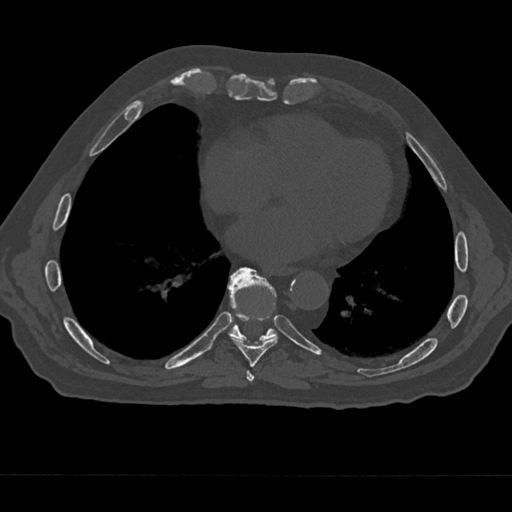
CT including the spine, one axial slice; slice 294 of 797 in the series (ordered by position); reconstruction kernel Br40s/3; 120 kVp; bone window (W 1800 / L 400 HU); 512 × 512 image matrix, field of view 377 × 377 mm. Patient: male, 75 years. From the clinical record (not read from this slice): primary cancer: renal; vertebrae with lytic lesions (as recorded): T4.
Structures marked on this image (semi-automatic segmentation, software-assisted and operator-edited):
- T7 vertebra: bounding box <244,370,257,385> (left, top, right, bottom; pixels)
- T8 vertebra: <231,283,279,367>
- T9 vertebra: <227,267,277,341>